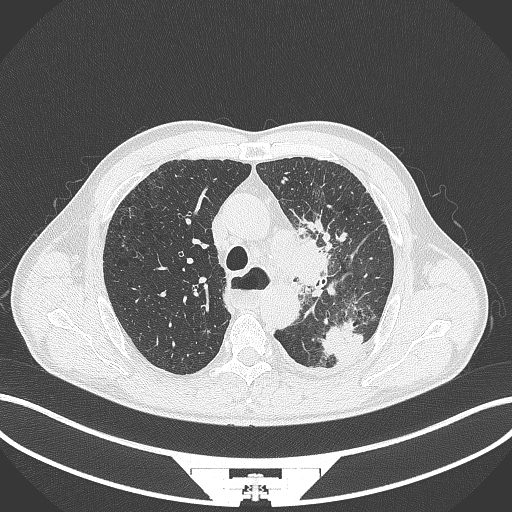
Chest CT, one axial slice; slice 278 of 411 in the series (ordered by position); reconstruction kernel B70f; 120 kVp; lung window (W 1500 / L -600 HU); 512 × 512 image matrix, field of view 400 × 400 mm. Patient: male, 57 years. Case-level facts recorded for this patient, not image findings: clinical TNM (as recorded): T2a N1 M0.
Outlined on this slice (bounding box drawn by a radiologist):
- lung tumour (recorded histology: squamous cell carcinoma): bounding box (x1, y1, x2, y2) in pixels: (290, 232, 336, 297)